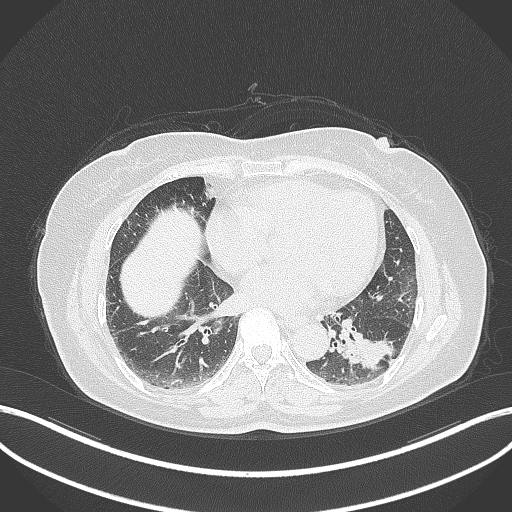
Chest CT, one axial slice. Reconstruction kernel B70f. 120 kVp. Lung window (W 1500 / L -600 HU). 512 × 512 image matrix, field of view 400 × 400 mm. Female patient, age 59 years. Case-level facts recorded for this patient, not image findings: clinical TNM (as recorded): T2a N0 M0.
Annotated regions visible in this slice (bounding box drawn by a radiologist):
- lung tumour (recorded histology: adenocarcinoma): bounding box (x1, y1, x2, y2) in pixels: (345, 321, 393, 372)